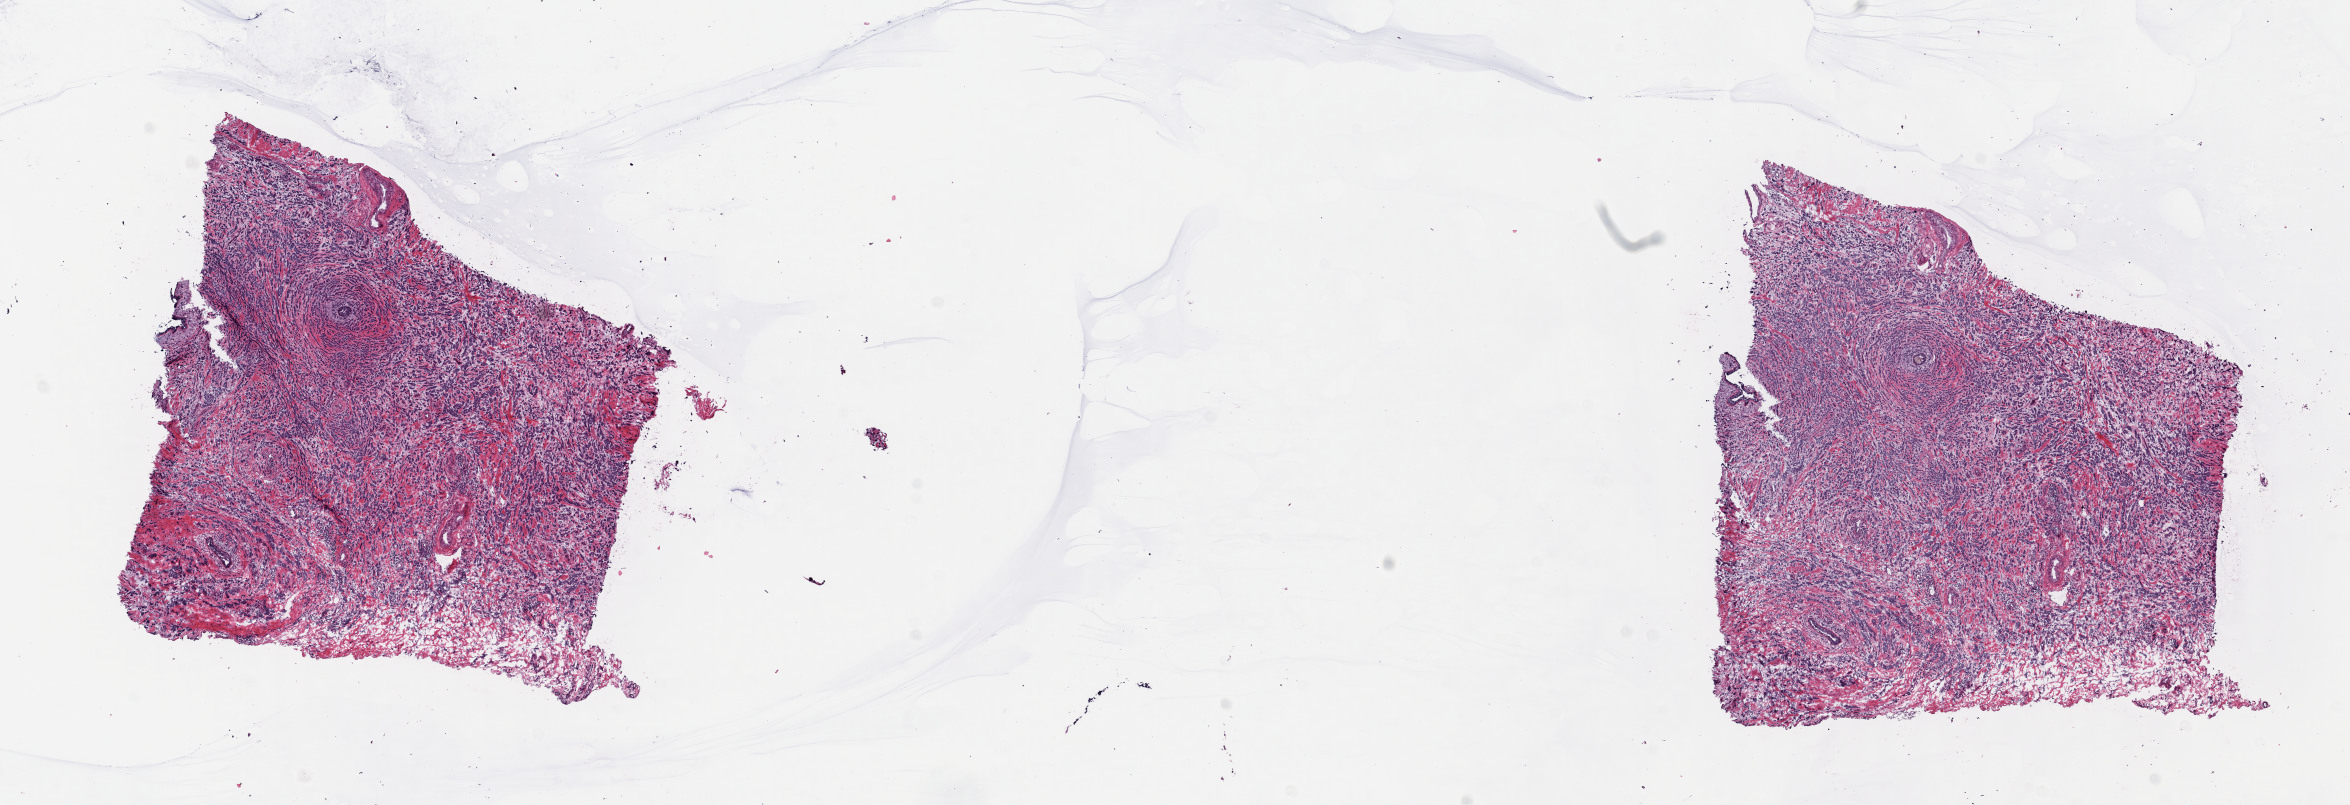
Whole-slide histology image, H&E-stained — low-resolution overview of the scanned area, about 18.5 x 6.3 mm (from a 40x scan). Frozen section from the top of the tissue portion. Breast, primary tumour sample. Female, age 65 years at initial diagnosis. Pathologist review of this section (percent, as recorded): tumour cells 85%, tumour nuclei 85%, normal cells 1%, stromal cells 14%, necrosis 0%. Inflammatory infiltration, as recorded: lymphocyte infiltration 2%, monocyte infiltration 1%, neutrophil infiltration 1%.
• pathologic diagnosis: Infiltrating duct carcinoma, NOS
• TNM: T1c N2a MX
• lymph nodes positive (case pathology): 9 of 15 examined
• AJCC pathologic stage: IIIA